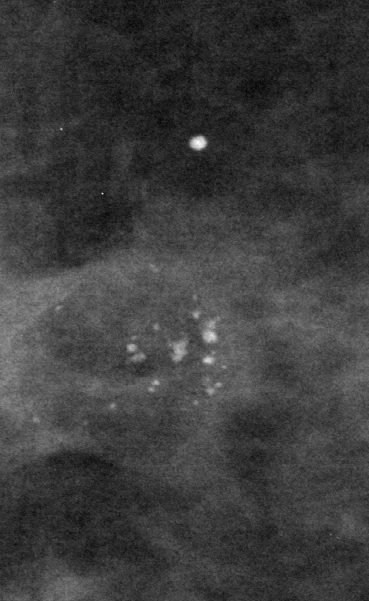
Crop from a digitized film mammogram around one marked abnormality, left breast, CC view.
- Calcifications, morphology amorphous, distribution clustered; BI-RADS assessment category 4; pathology result (as recorded, not read from the image): benign.